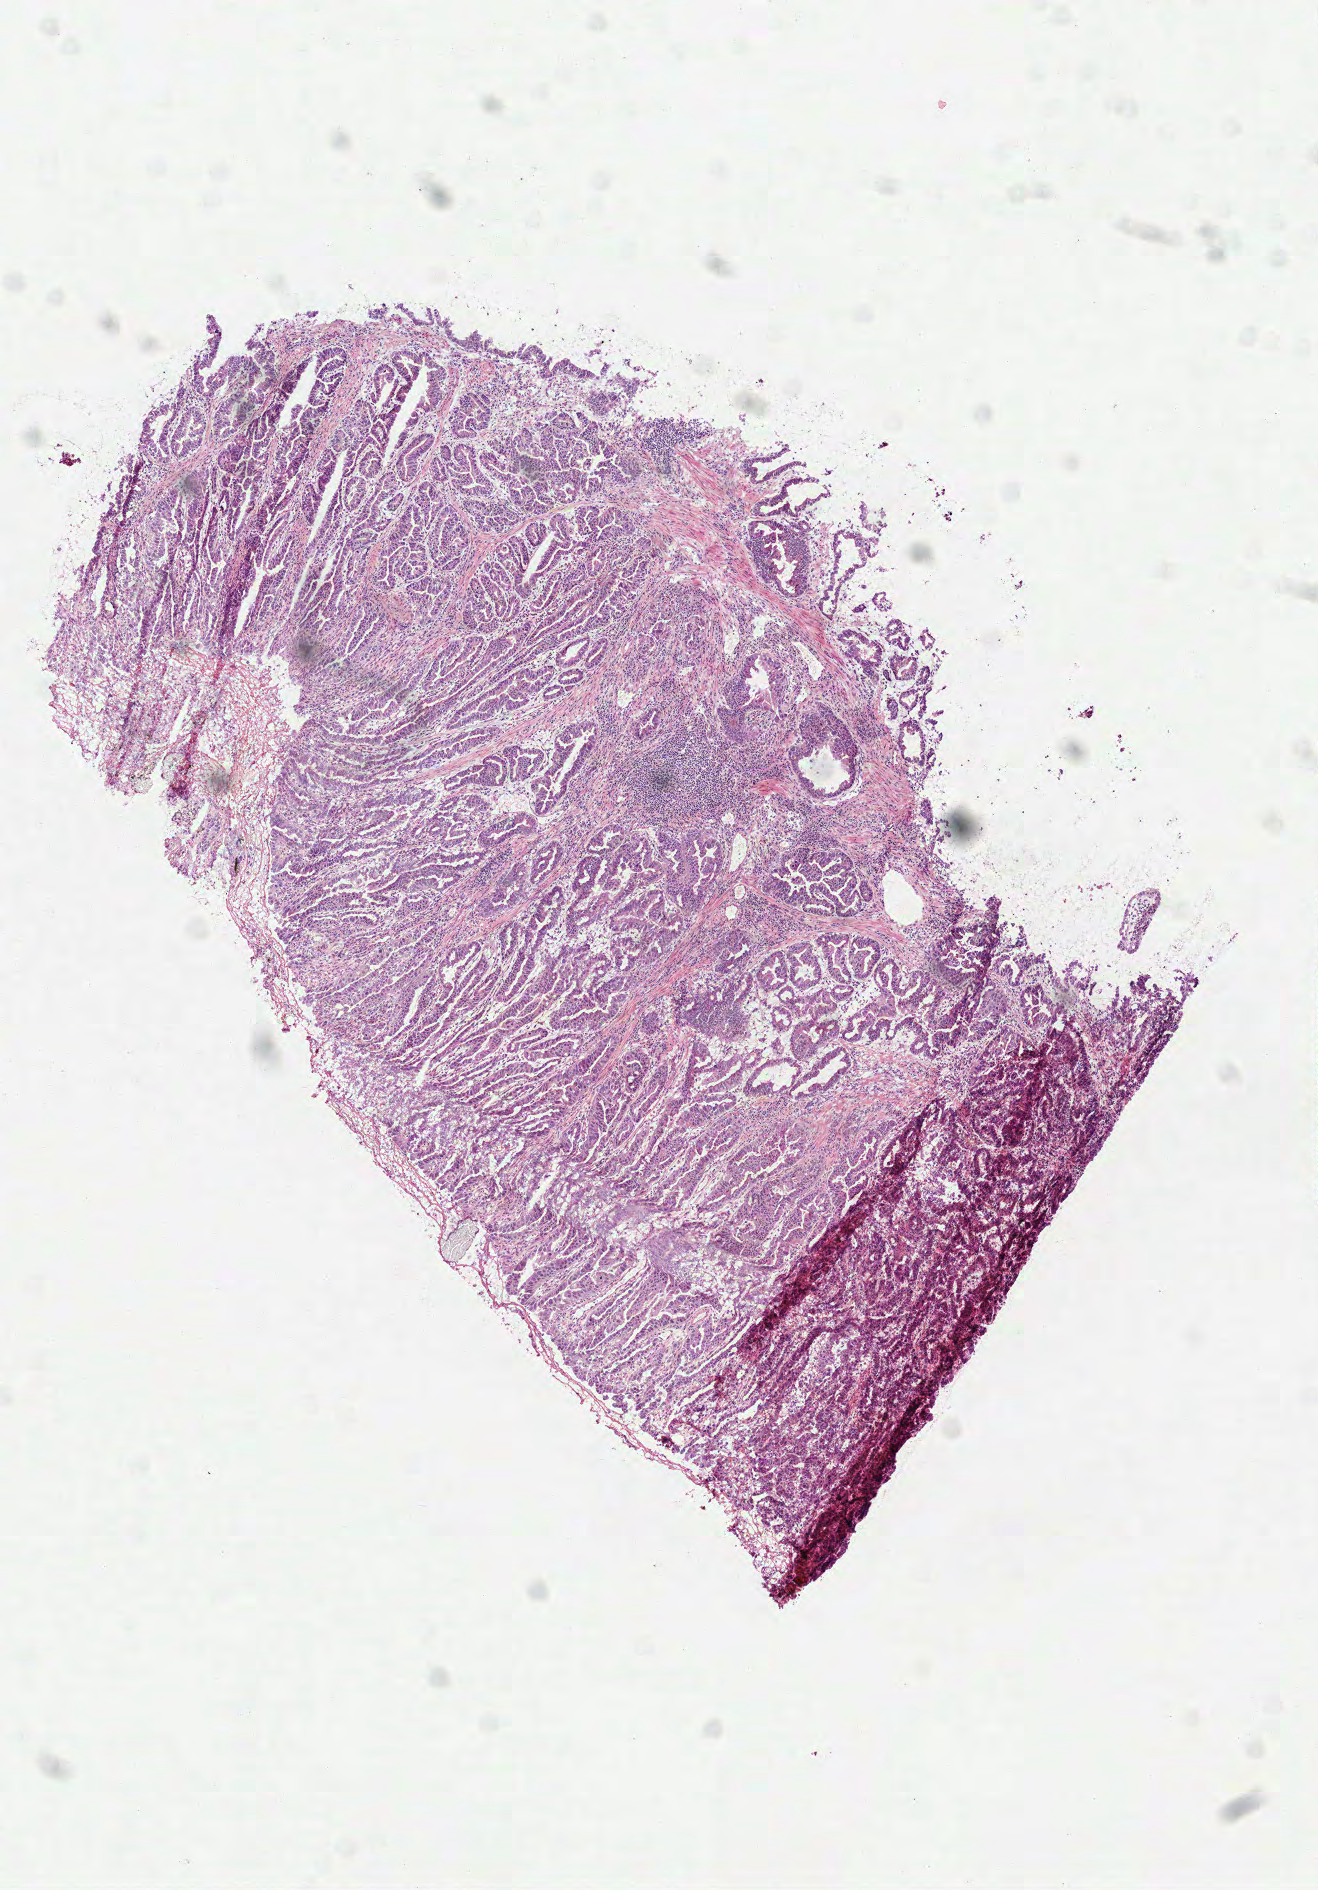
Whole-slide histology image, H&E-stained, a low-resolution overview of the entire scanned area, about 5.3 x 7.6 mm, frozen section, sample: primary tumour, stomach. Male, age 62 years at initial diagnosis. Histologic grade: G2 (moderately differentiated). Pathologist review of this section (percent, as recorded): tumour cells 80%, tumour nuclei 75%, normal cells 5%, stromal cells 15%, necrosis 0%.
AJCC pathologic stage: II (6th edition). Pathologic diagnosis: Papillary adenocarcinoma, NOS (cardia, NOS).